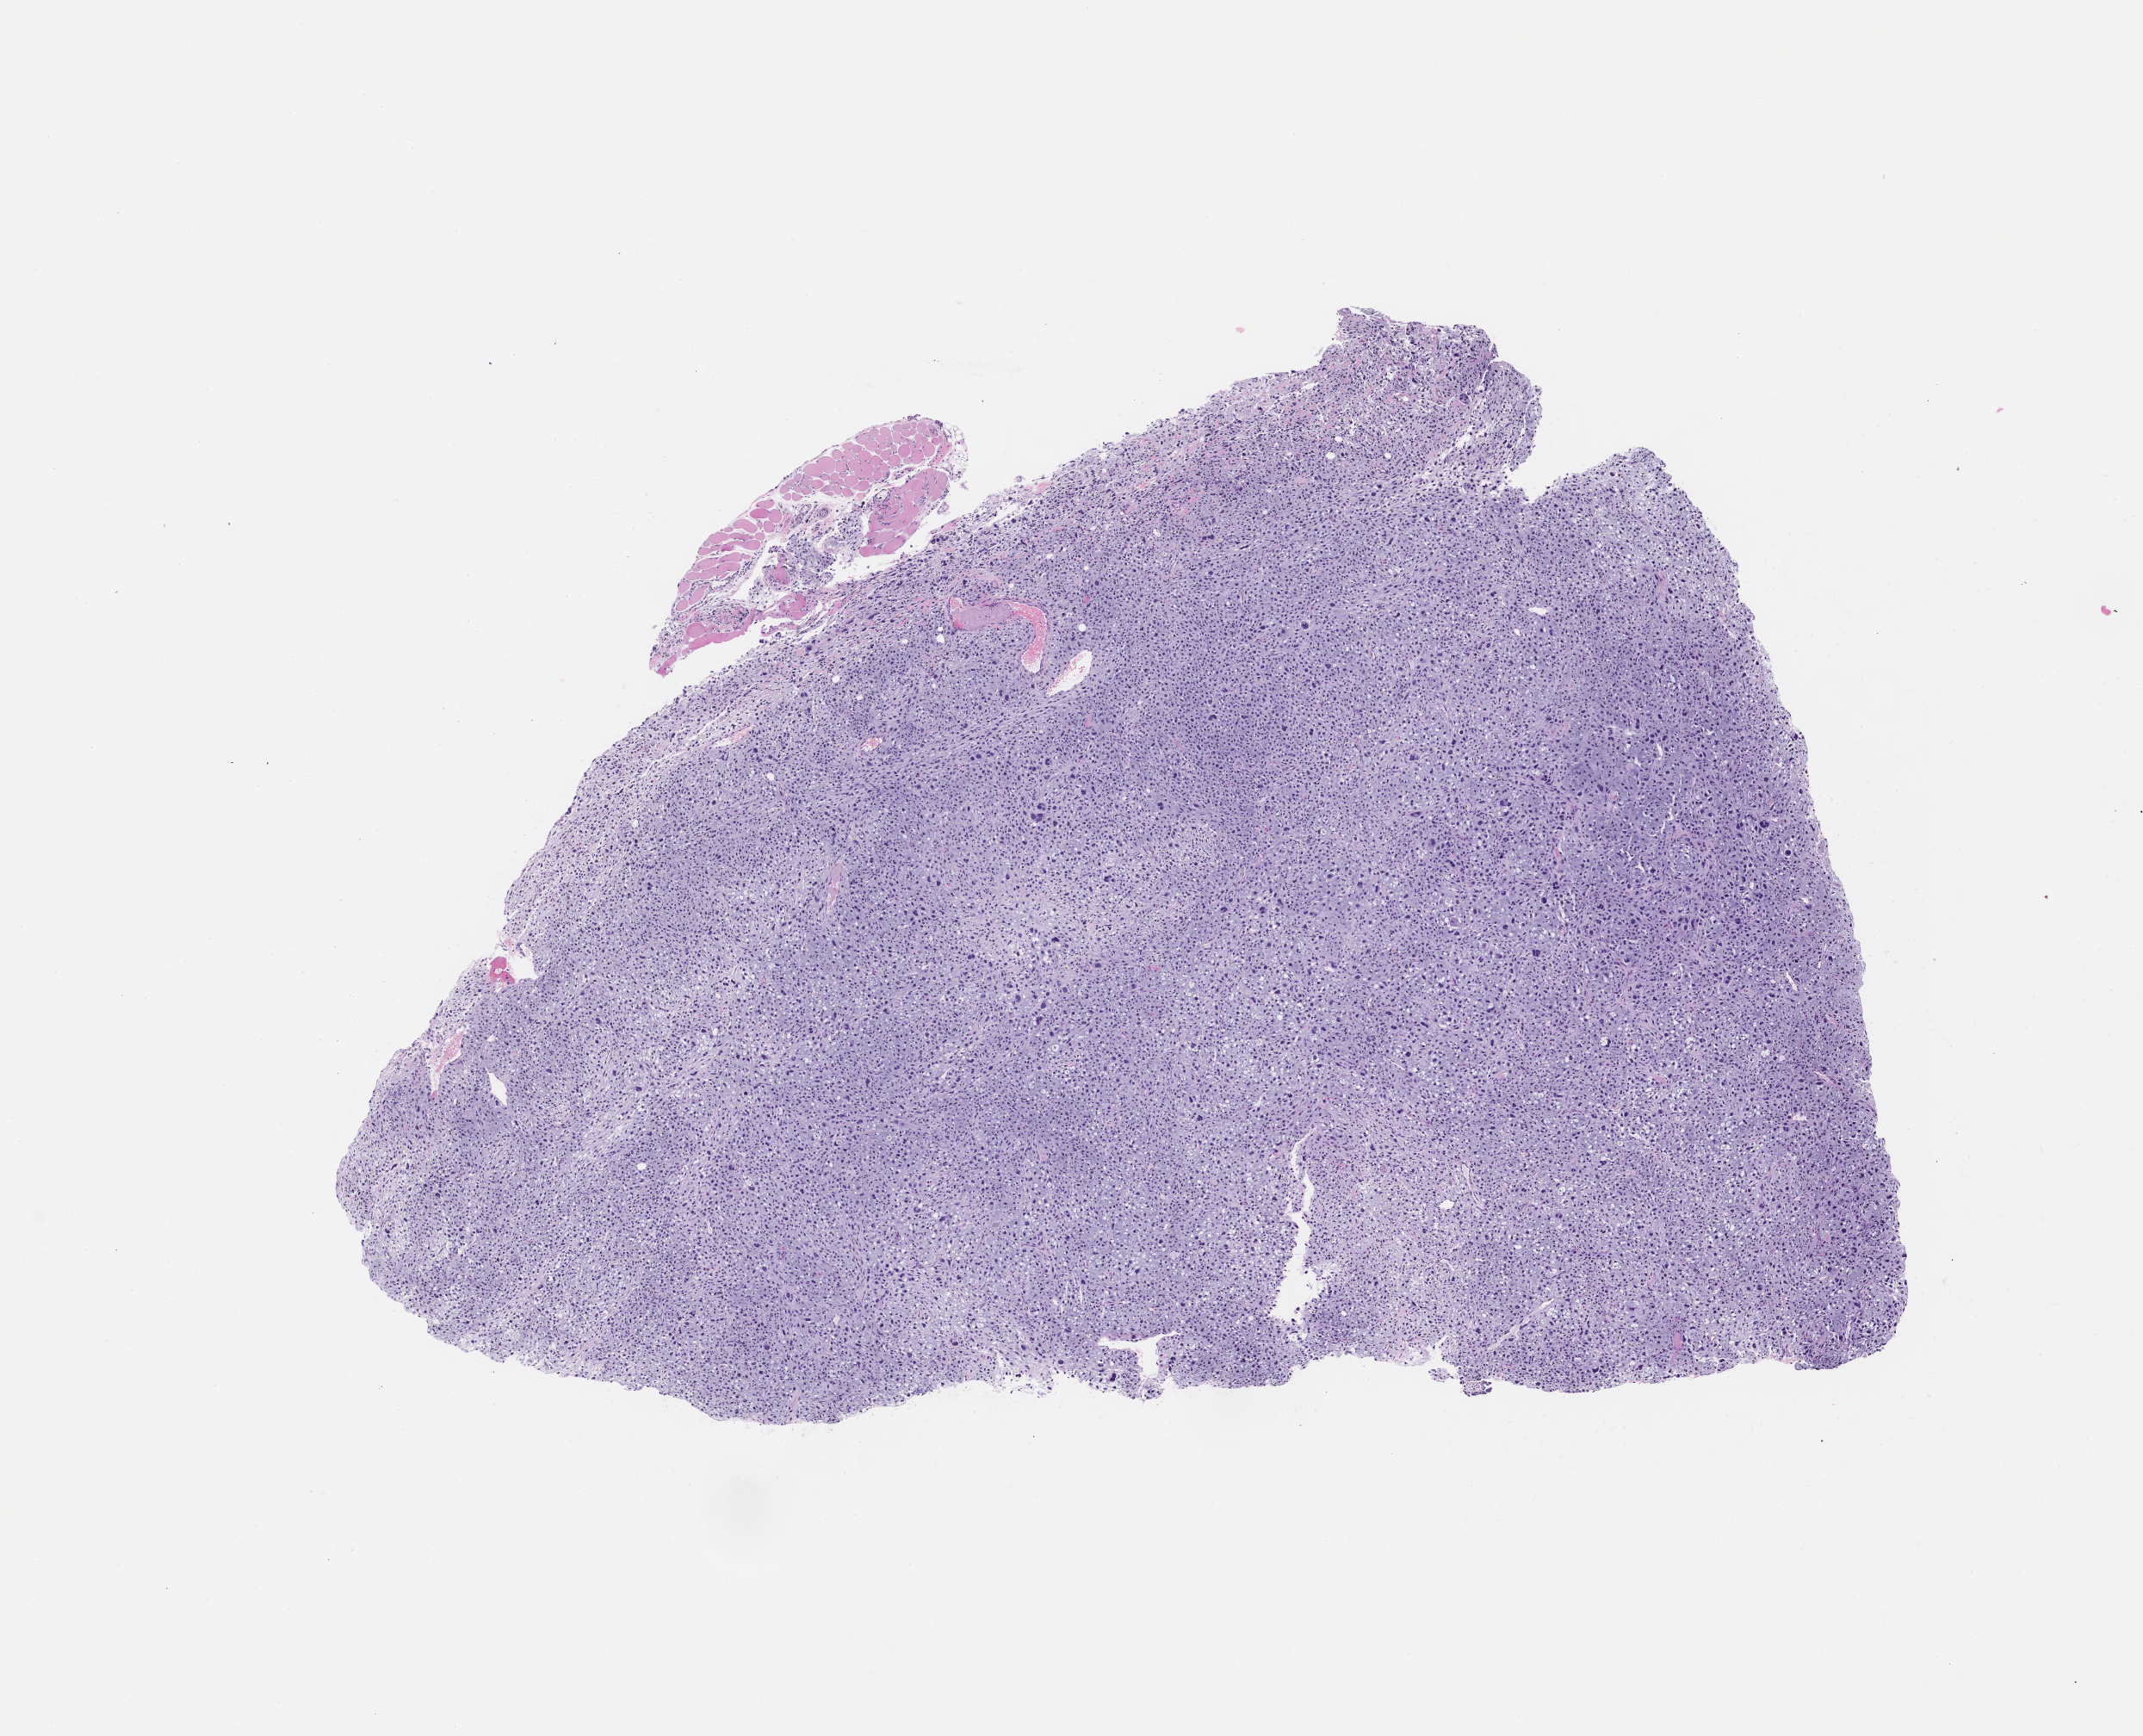
Whole-slide image, hematoxylin and eosin (H&E): patient-derived xenograft (human tumor grown in a mouse), passage 0 — whole scanned area (about 10.0 x 8.1 mm) shown as a low-resolution overview; formalin-fixed, paraffin-embedded (FFPE) tissue; originating tumor site category: musculoskeletal.
Originating patient diagnosis: Myxofibrosarcoma.